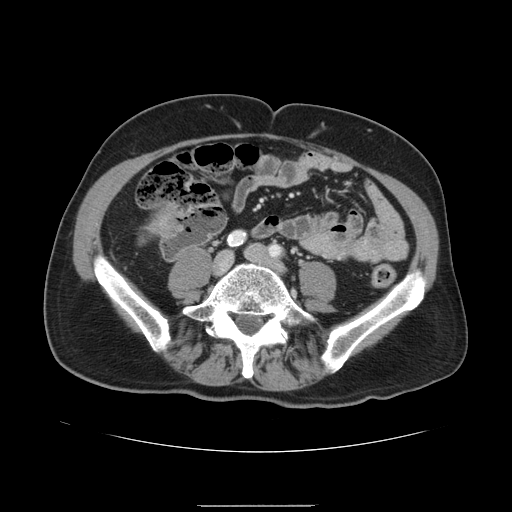
Contrast-enhanced abdominal CT, one axial slice. Position 5 of 168 along the scan axis. Intravenous contrast given. Soft-tissue window (W 400 / L 40 HU). 2.5 mm slice thickness. 512 × 512 image matrix, field of view 386 × 386 mm. Male patient, age 74 years. Case-level facts recorded for this patient, not image findings: diagnosis: colorectal cancer liver metastases, imaged before liver resection; multiple liver metastases: no.
Annotated regions visible in this slice (manually delineated by an expert):
- liver: bounding box [x1, y1, x2, y2] px = [144, 203, 185, 239]